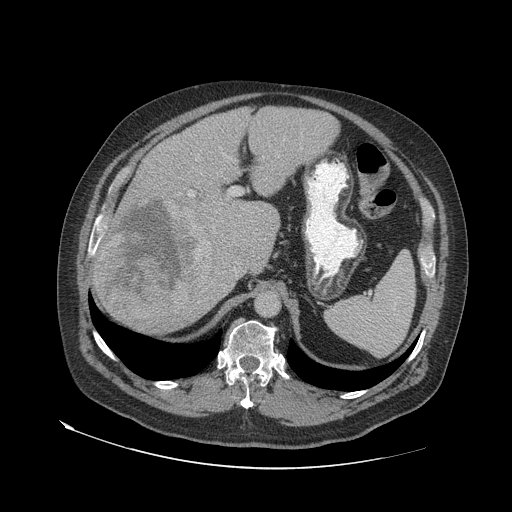
Contrast-enhanced abdominal CT (liver protocol), one axial slice; slice 44 of 79 in the series (ordered by position); soft-tissue window (W 400 / L 40 HU); 2.5 mm slice thickness; 512 × 512 image matrix. From the clinical record (not read from this slice): diagnosis: hepatocellular carcinoma (patient treated with transarterial chemoembolisation; whether this scan precedes or follows treatment is not stated here); TNM stage (as recorded): Stage-IVA.
Structures marked on this image (semi-automatic segmentation, software-assisted and operator-edited):
- liver parenchyma outside the tumour (the mass and vessels are separate outlines, so this box may not span the whole liver): bounding box (x1, y1, x2, y2) in pixels: (92, 106, 338, 332)
- mass: (98, 197, 214, 318)
- liver vessels: (92, 159, 235, 270)